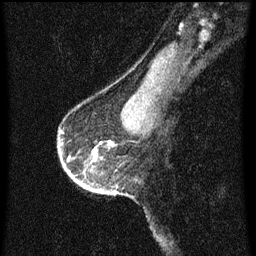
Breast MRI (dynamic contrast-enhanced), one sagittal slice. Position 48 of 60 along the scan axis. Dynamic contrast-enhanced series, image 2 of 3 at this slice position (ordered by acquisition). 1.5 T. TE 4.2 ms, TR 8 ms. 2 mm slice thickness. 256 × 256 image matrix, field of view 180 × 180 mm. Patient: female, 56 years.
Outlined on this slice (semi-automatic segmentation, software-assisted and operator-edited):
- analysis volume of interest (the breast-tissue region the enhancement analysis was run in; not a lesion): bounding box (x1, y1, x2, y2) in pixels: (58, 130, 119, 195)
- tumour enhancement mask (voxels above the 70 % enhancement threshold inside the analysis volume of interest): (68, 150, 115, 195)